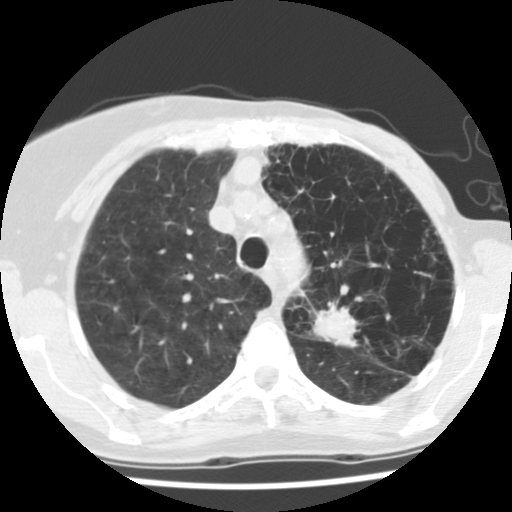
Low-dose screening chest CT, one axial slice; position 98 of 128 along the scan axis; 140 kVp; lung window (W 1500 / L -600 HU); 2.5 mm slice thickness; 512 × 512 image matrix, field of view 290 × 290 mm.
Structures marked on this image (manually delineated by an expert):
- lesion 1 (tumor, upper lobe of left lung): bounding box <313,301,358,348> (left, top, right, bottom; pixels)